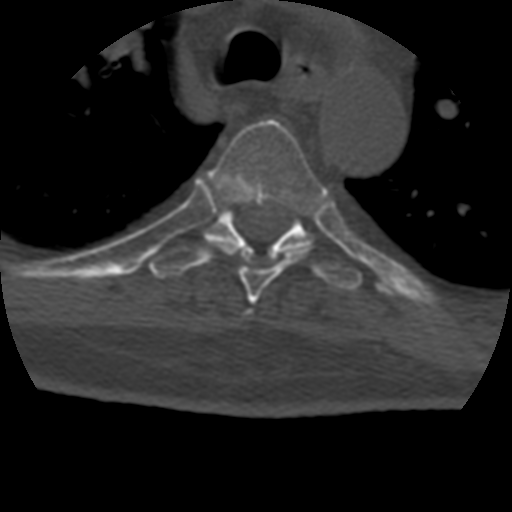
CT including the spine, one axial slice; slice 312 of 399 in the series (ordered by position); reconstruction kernel STANDARD; 120 kVp; bone window (W 1800 / L 400 HU); 1.25 mm slice thickness; 512 × 512 image matrix. Patient age 69 years. Case-level facts recorded for this patient, not image findings: primary cancer: prostate.
Structures marked on this image (semi-automatic segmentation, software-assisted and operator-edited):
- T5 vertebra: bounding box <204,119,327,305> (left, top, right, bottom; pixels)
- T6 vertebra: <149,207,363,290>